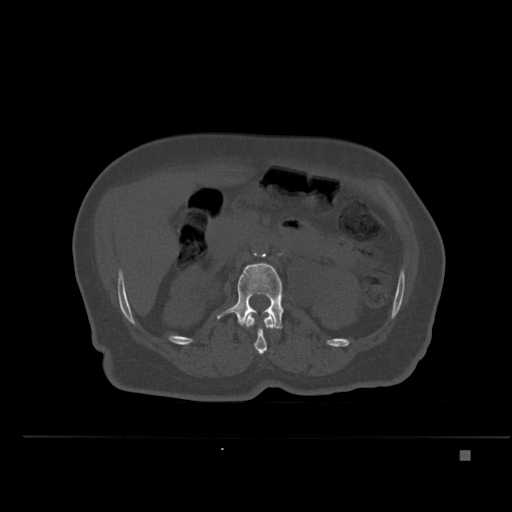
CT including the spine, one axial slice. Slice 222 of 477 in the series (ordered by position). Bone window (W 1800 / L 400 HU). 512 × 512 image matrix, field of view 422 × 422 mm. Female patient, age 74 years. Case-level facts recorded for this patient, not image findings: primary cancer: colon.
Structures marked on this image (semi-automatic segmentation, software-assisted and operator-edited):
- L1 vertebra: bounding box [x1, y1, x2, y2] px = [244, 313, 276, 354]
- L2 vertebra: [217, 263, 284, 329]